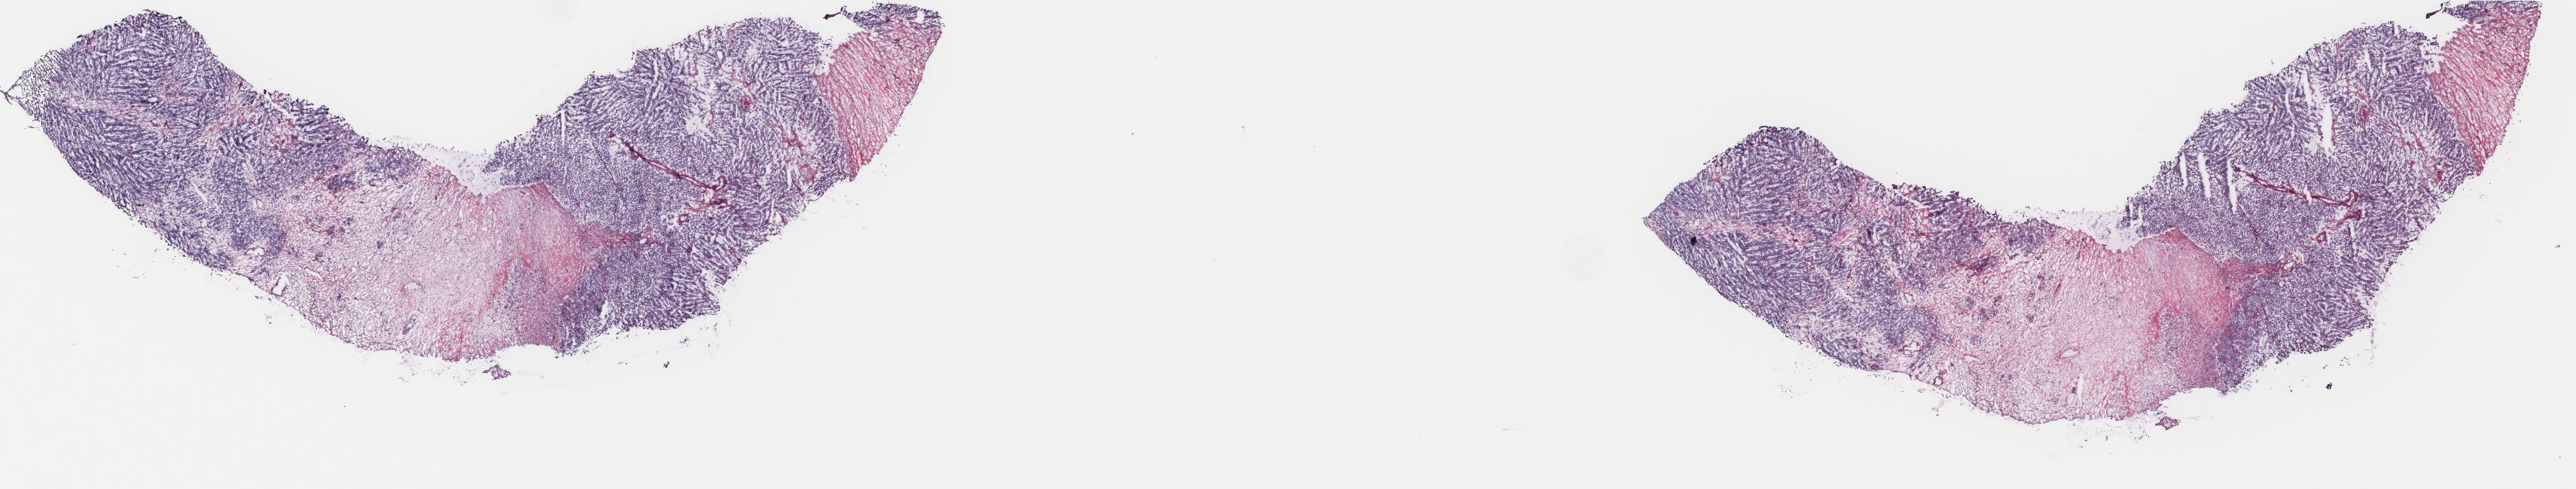
Digitized H&E tissue section (whole slide) — low-resolution overview of the scanned area, about 27.2 x 5.2 mm (slide scanned at 40x). Frozen section. Testis, primary tumour sample. Male patient; age at initial diagnosis 26 years. Pathologist review of this section (percent, as recorded): tumour cells 75%, tumour nuclei 75%, normal cells 0%, stromal cells 24%, necrosis 1%. Infiltration values recorded for this section: lymphocyte infiltration 5%, monocyte infiltration 1%, neutrophil infiltration 1%.
AJCC pathologic stage: IS (7th edition). Diagnosis: Mixed germ cell tumor.